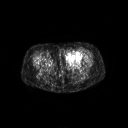
FDG PET of an extremity soft-tissue mass (from a PET/CT study), one axial slice; position 28 of 267 along the scan axis; 128 × 128 image matrix, field of view 700 × 700 mm. Patient: female, 47 years. Case-level facts recorded for this patient, not image findings: histological type: myxofibrosarcoma; grade: intermediate; site of the primary tumour: left thigh.
Structures marked on this image (expert contour drawn on MRI and transferred to this co-registered scan by the dataset authors):
- gross tumour volume including surrounding oedema: box from (x=65, y=51) to (x=82, y=65) px
- gross tumour volume (mass): (x=65, y=51)–(x=82, y=64)